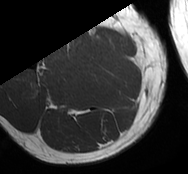
MRI of an extremity soft-tissue mass, one axial slice. Slice 17 of 93 in the series (ordered by position). MR volume resampled by the dataset authors to the PET/CT grid (not the native acquisition matrix). 3.27 mm slice thickness. 188 × 174 image matrix, field of view 184 × 170 mm. Male patient. Case-level facts recorded for this patient, not image findings: histological type: undifferentiated - pleiomorphic; grade: high; site of the primary tumour: right thigh.
Annotated regions visible in this slice (expert contour drawn on MRI and transferred to this co-registered scan by the dataset authors):
- gross tumour volume including surrounding oedema: bounding box <58,44,76,65> (left, top, right, bottom; pixels)